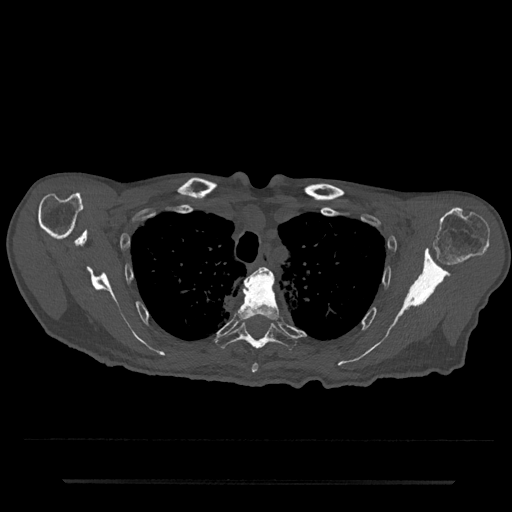
CT including the spine, one axial slice. Slice 602 of 797 in the series (ordered by position). Reconstruction kernel Br40s/3. Bone window (W 1800 / L 400 HU). 0.5 mm slice thickness. 512 × 512 image matrix, field of view 427 × 427 mm. Male patient, age 74 years. Case-level facts recorded for this patient, not image findings: primary cancer: prostate.
Structures marked on this image (semi-automatic segmentation, software-assisted and operator-edited):
- T3 vertebra: bounding box (x1, y1, x2, y2) in pixels: (263, 268, 273, 277)
- T4 vertebra: (237, 268, 280, 373)
- T5 vertebra: (215, 318, 297, 351)